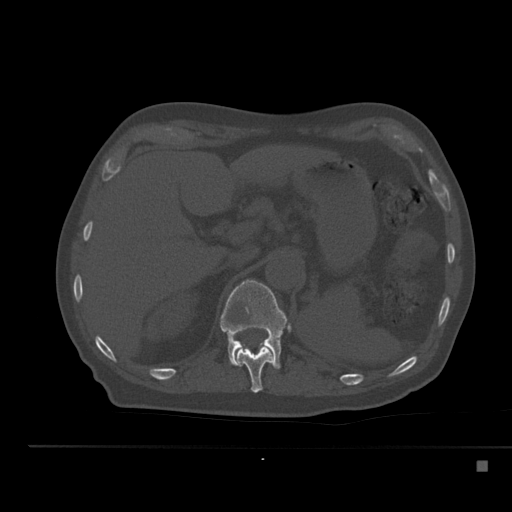
CT including the spine, one axial slice; position 238 of 517 along the scan axis; reconstruction kernel Br40s; 120 kVp; bone window (W 1800 / L 400 HU); 1.5 mm slice thickness; 512 × 512 image matrix, field of view 408 × 408 mm. Male patient, age 70 years. Case-level facts recorded for this patient, not image findings: primary cancer: renal; vertebrae with lytic lesions (as recorded): T4, T6, T10, T12, L3, L4, L5.
Structures marked on this image (semi-automatically segmented with operator editing):
- T11 vertebra: bounding box [x1, y1, x2, y2] px = [235, 345, 274, 393]
- T12 vertebra: [220, 280, 289, 369]